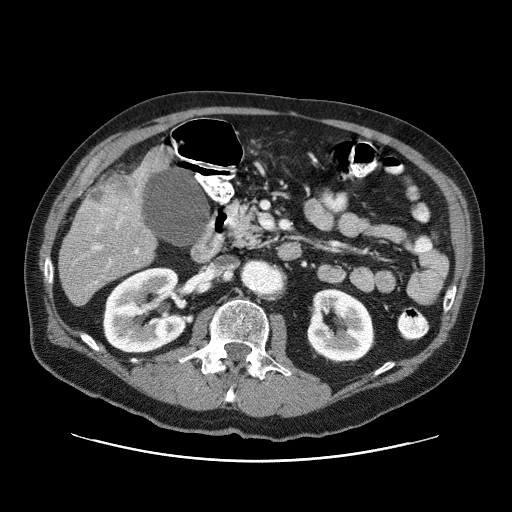
Contrast-enhanced abdominal CT (liver protocol), one axial slice. Position 22 of 87 along the scan axis. Reconstruction kernel STANDARD. 120 kVp. One of 3 acquisitions stored at this slice position. Soft-tissue window (W 400 / L 40 HU). 2.5 mm slice thickness. 512 × 512 image matrix, field of view 400 × 400 mm. From the clinical record (not read from this slice): diagnosis: hepatocellular carcinoma (patient treated with transarterial chemoembolisation; whether this scan precedes or follows treatment is not stated here); TNM stage (as recorded): Stage-IIIA; Child-Pugh class: A; tumour differentiation: well differentiated; tumour nodularity: multinodular.
Structures marked on this image (semi-automatic segmentation, software-assisted and operator-edited):
- liver parenchyma outside the tumour (the mass and vessels are separate outlines, so this box may not span the whole liver): bounding box [x1, y1, x2, y2] px = [58, 148, 168, 305]
- mass: [82, 174, 142, 224]
- liver vessels: [93, 174, 143, 284]